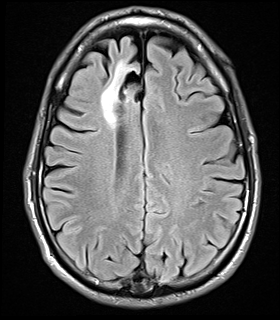
Brain MRI from a brain-tumour surgery series, one axial slice. Position 11 of 32 along the scan axis. T2 FLAIR. 5 mm slice thickness. 280 × 320 image matrix. From the clinical record (not read from this slice): histopathology: Glial fibroma; tumour location: Right Frontal.
Annotated regions visible in this slice (manually delineated by an expert):
- tumour: box from (x=101, y=61) to (x=141, y=127) px